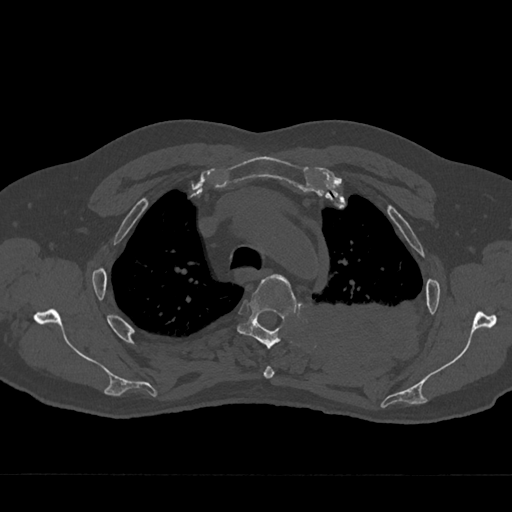
CT including the spine, one axial slice. Position 529 of 797 along the scan axis. Bone window (W 1800 / L 400 HU). 0.5 mm slice thickness. 512 × 512 image matrix, field of view 377 × 377 mm. Male patient, age 75 years. Case-level facts recorded for this patient, not image findings: primary cancer: renal.
Structures marked on this image (semi-automatically segmented with operator editing):
- T3 vertebra: bounding box <263,366,275,379> (left, top, right, bottom; pixels)
- T4 vertebra: <237,274,297,348>